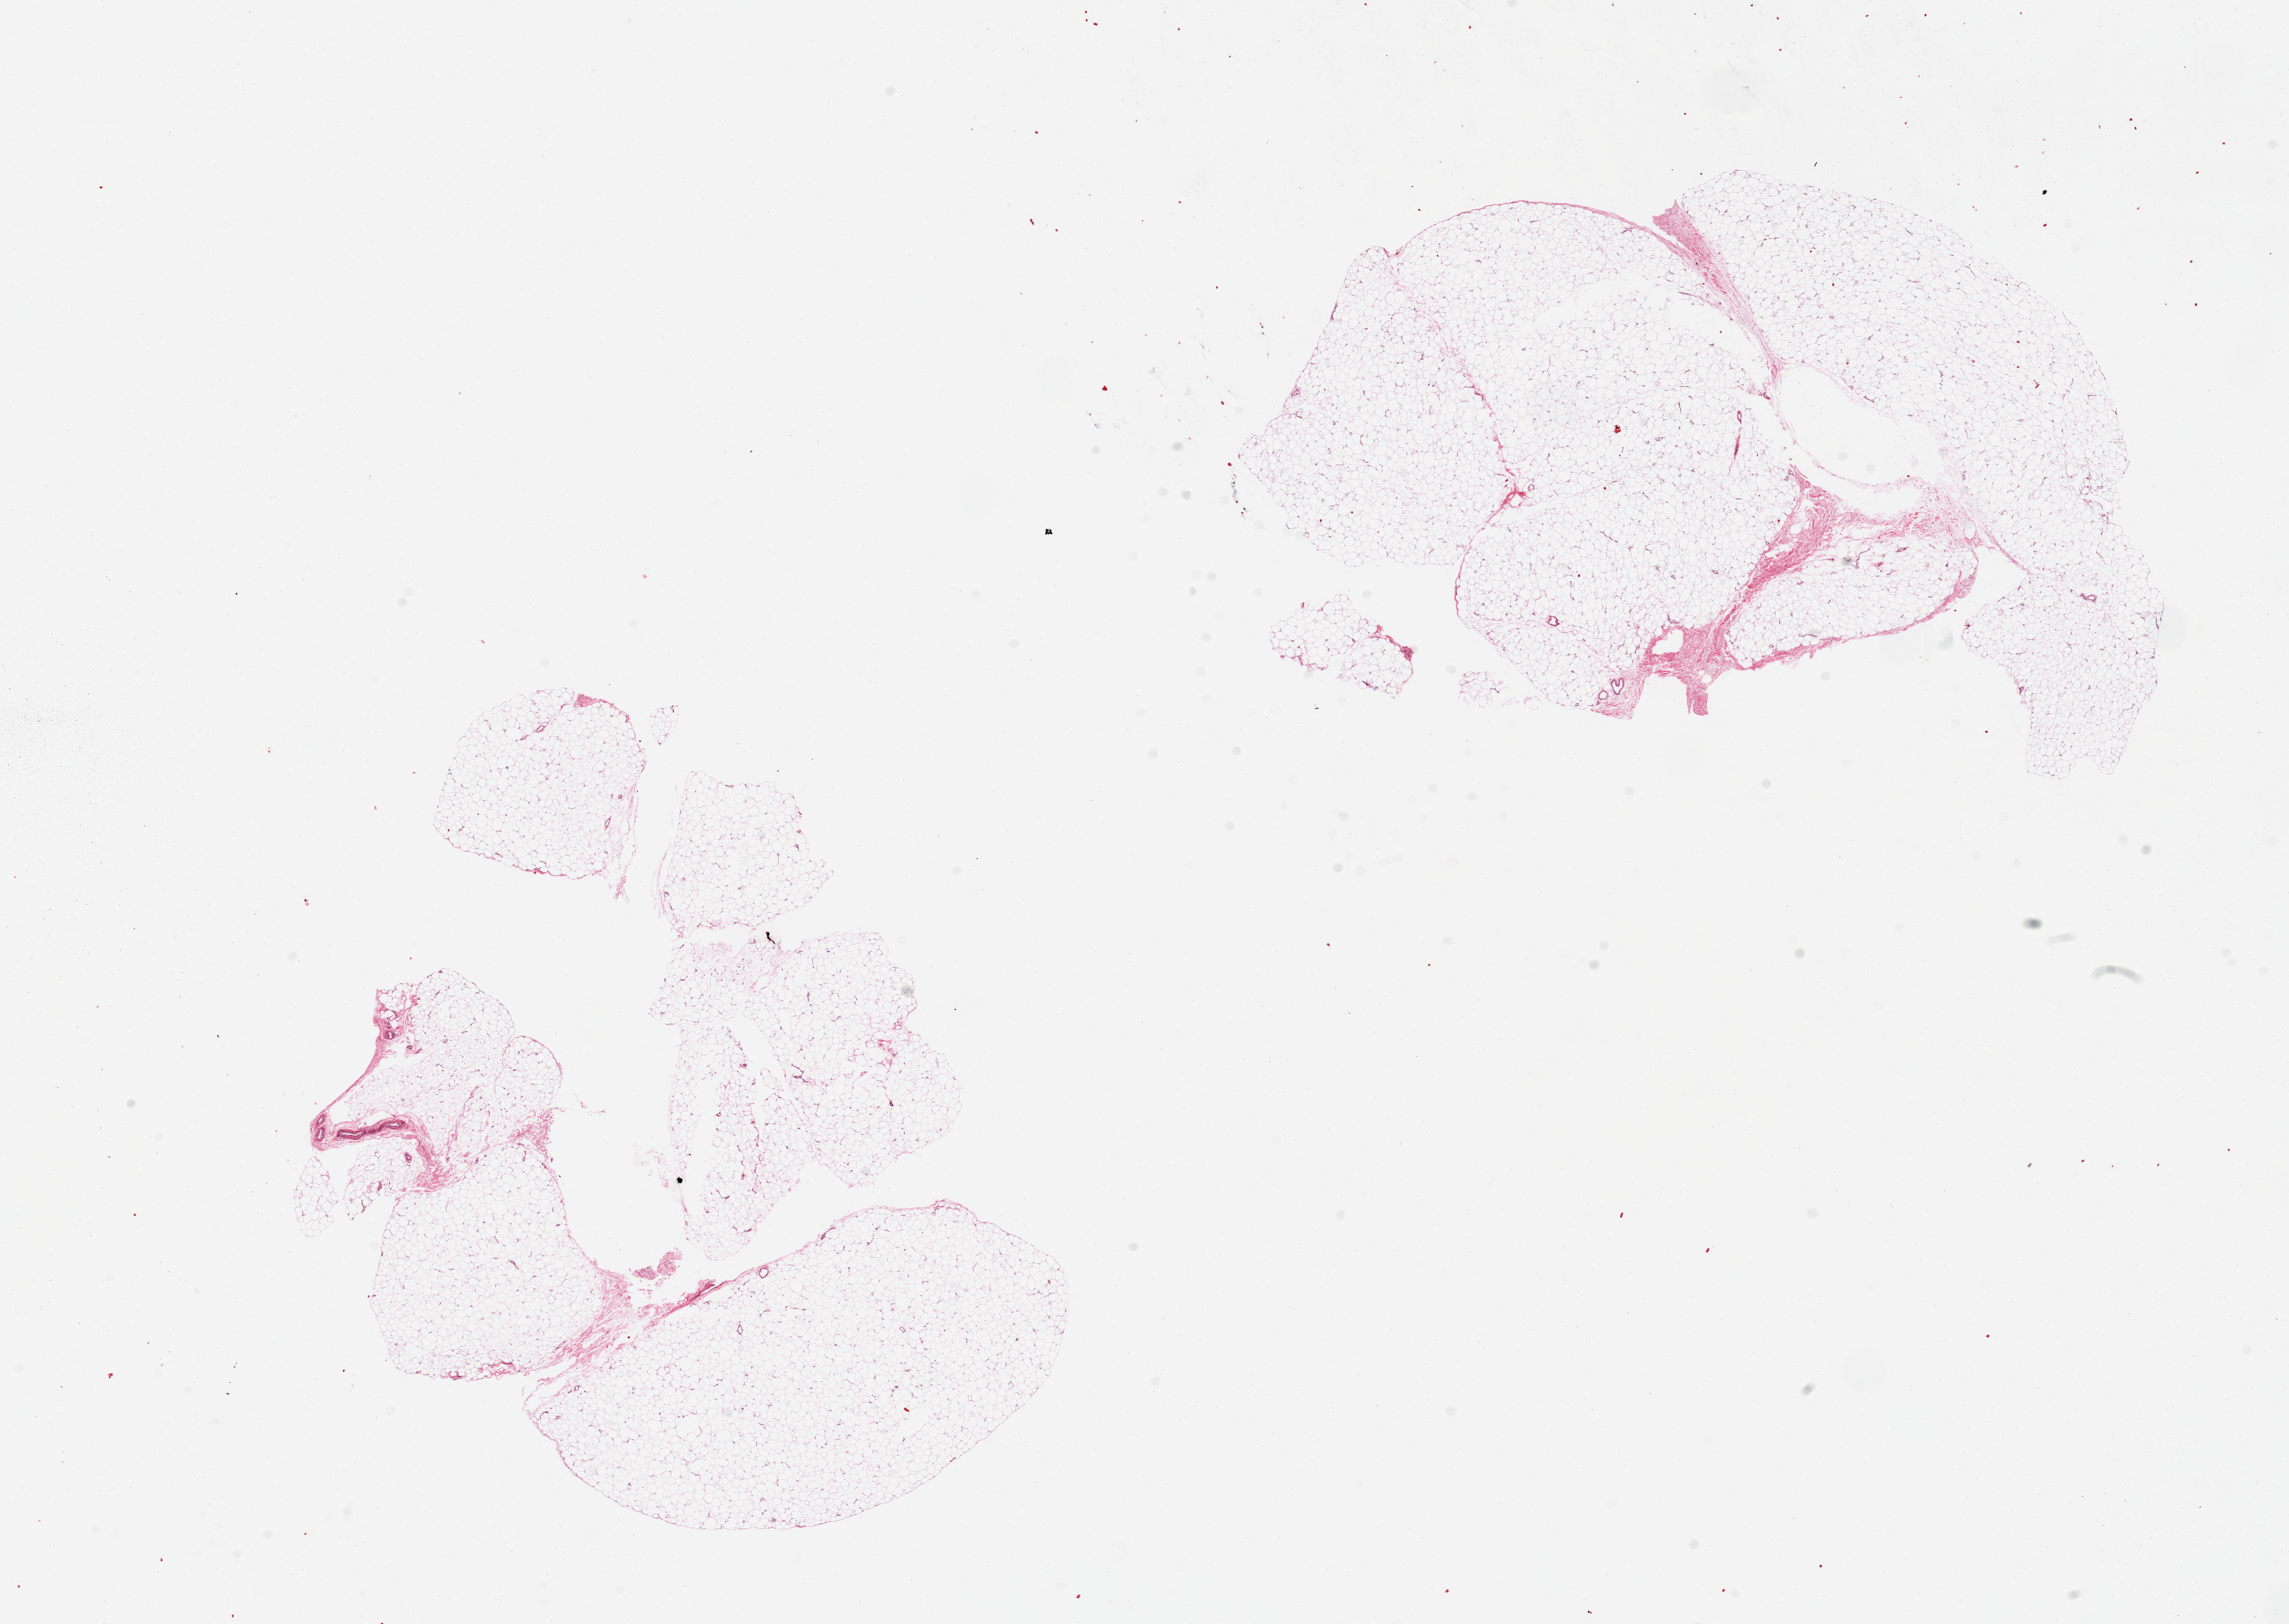
Whole-slide image, hematoxylin and eosin (H&E) stain — shown as a low-resolution overview of the whole scanned area (about 24.6 x 17.5 mm, acquisition: 20x scan). PAXgene-fixed paraffin-embedded (PFPE) section. Target tissue: adipose tissue. Tissue donor sample. Donor: female.
Reviewer comment on this tissue sample: 2 pieces, <10% is fibrous/vascular.